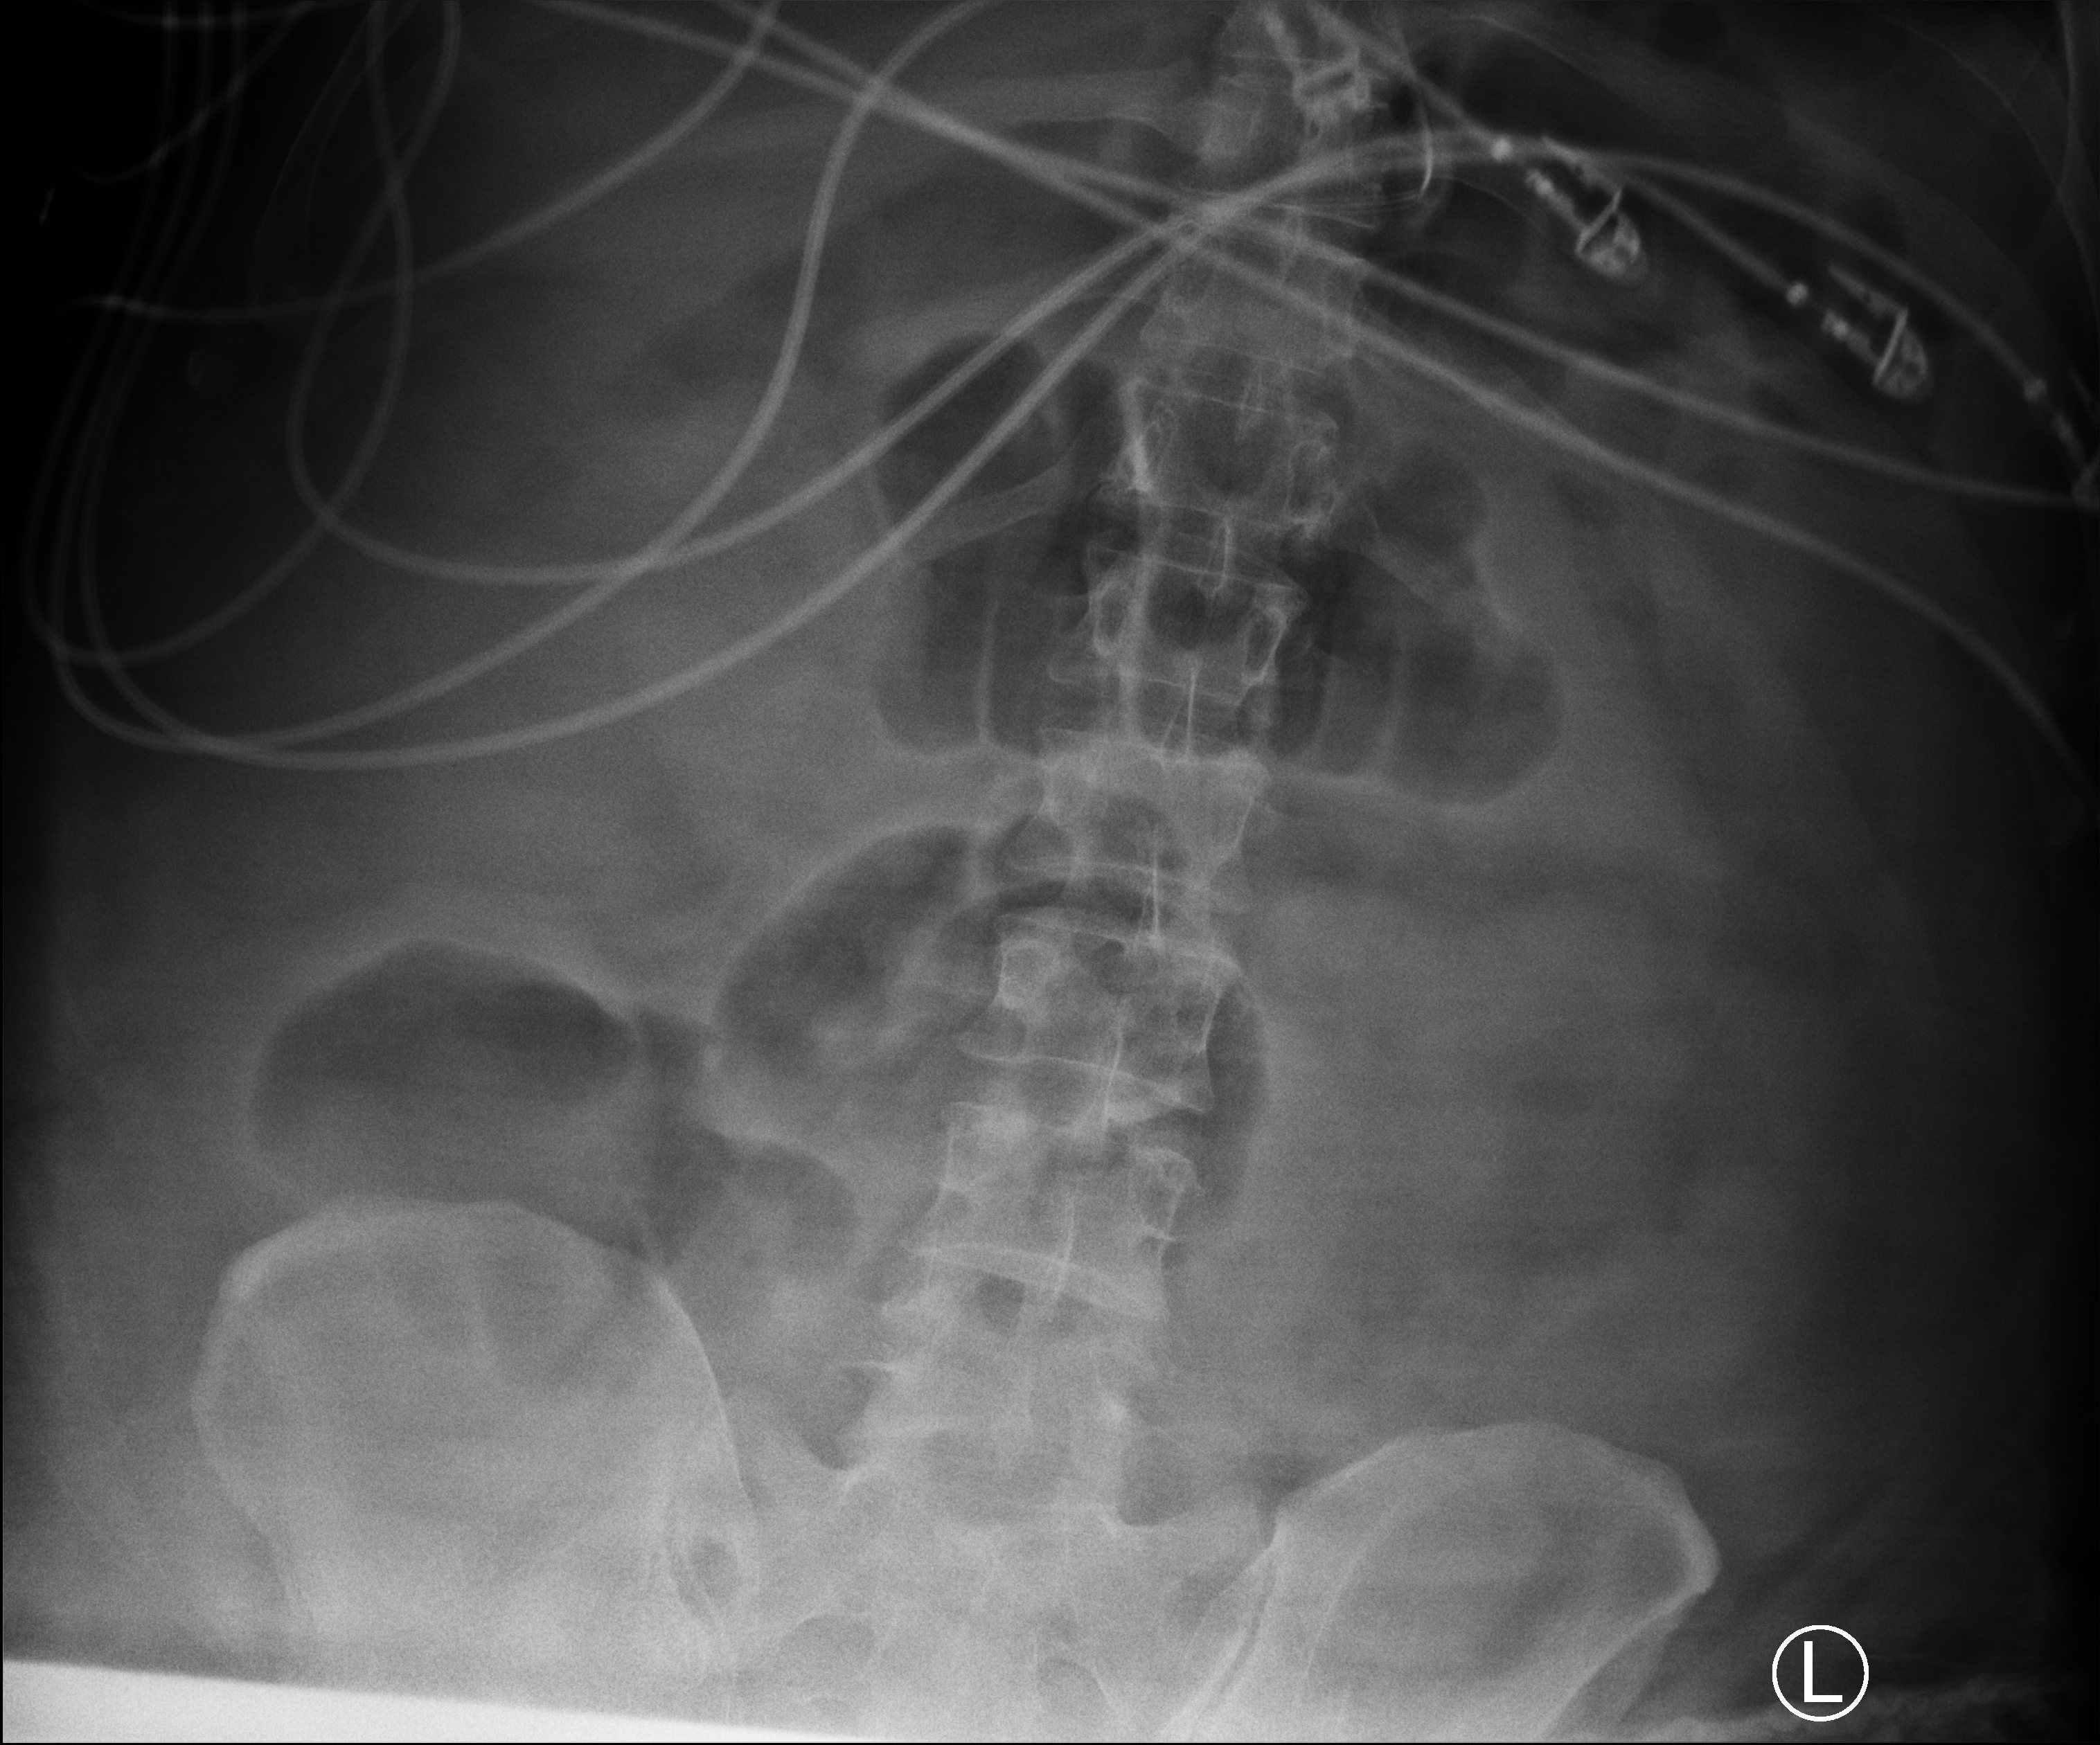
Portable abdomen radiograph. Patient hospitalised with COVID-19, aged 18–59 years.
Admission-level facts for this patient (not findings on this image; timing relative to this image not recorded):
- diabetes (admission record): no
- mechanically ventilated during this hospital stay: yes